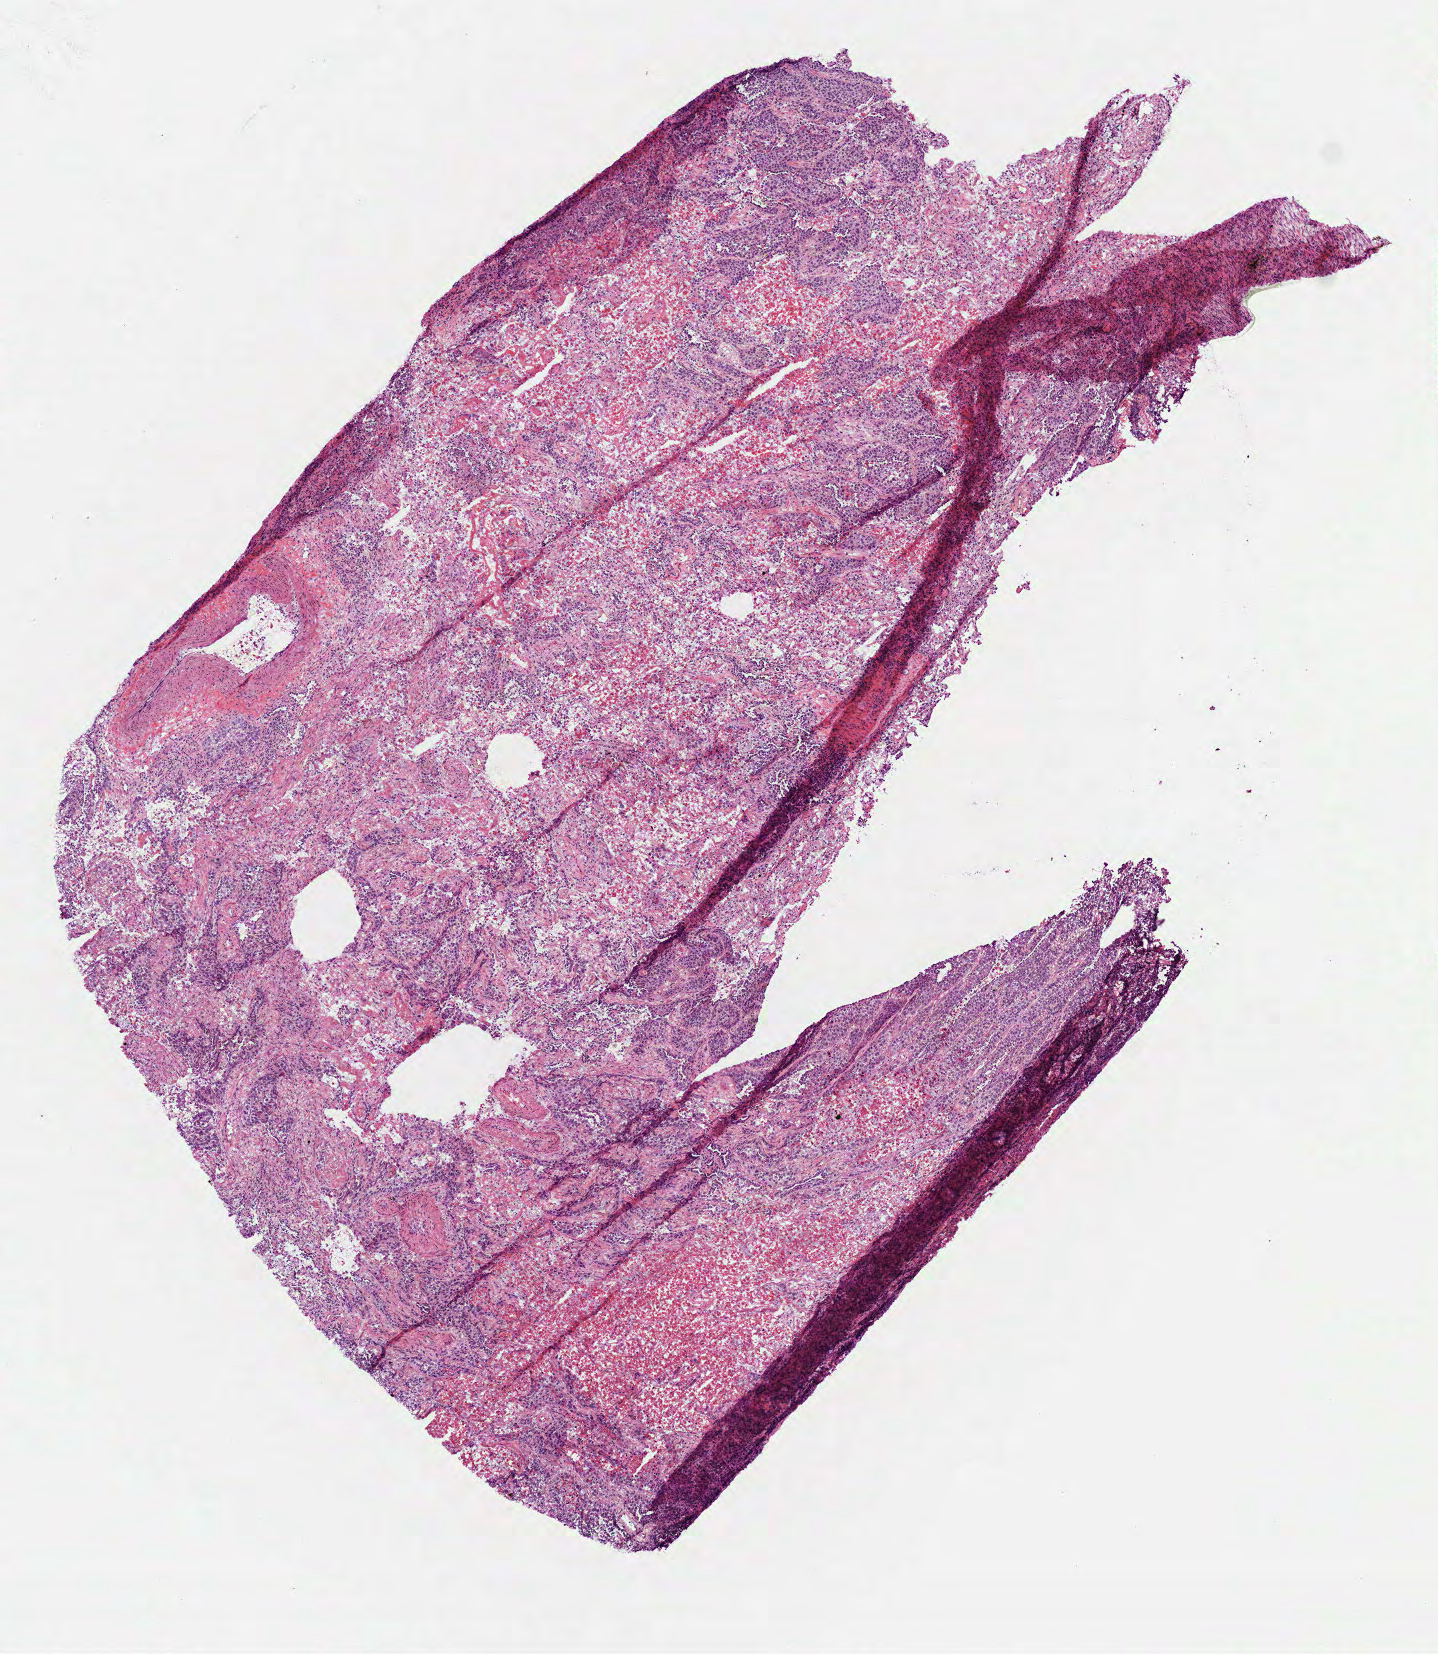
Whole-slide histology image, H&E — low-resolution overview of the scanned area, about 5.8 x 6.7 mm (slide scanned at 40x), frozen section from the top of the tissue portion, sample: primary tumour, lung. Patient: female, age at initial diagnosis 59 years. Composition of this section per pathologist review: tumour cells 85%, tumour nuclei 70%, normal cells 0%, stromal cells 15%, necrosis 0%.
TNM: T2 N0 M0. AJCC pathologic stage: IB (6th edition). Diagnosis: Squamous cell carcinoma, NOS (upper lobe, lung). Laterality: left.